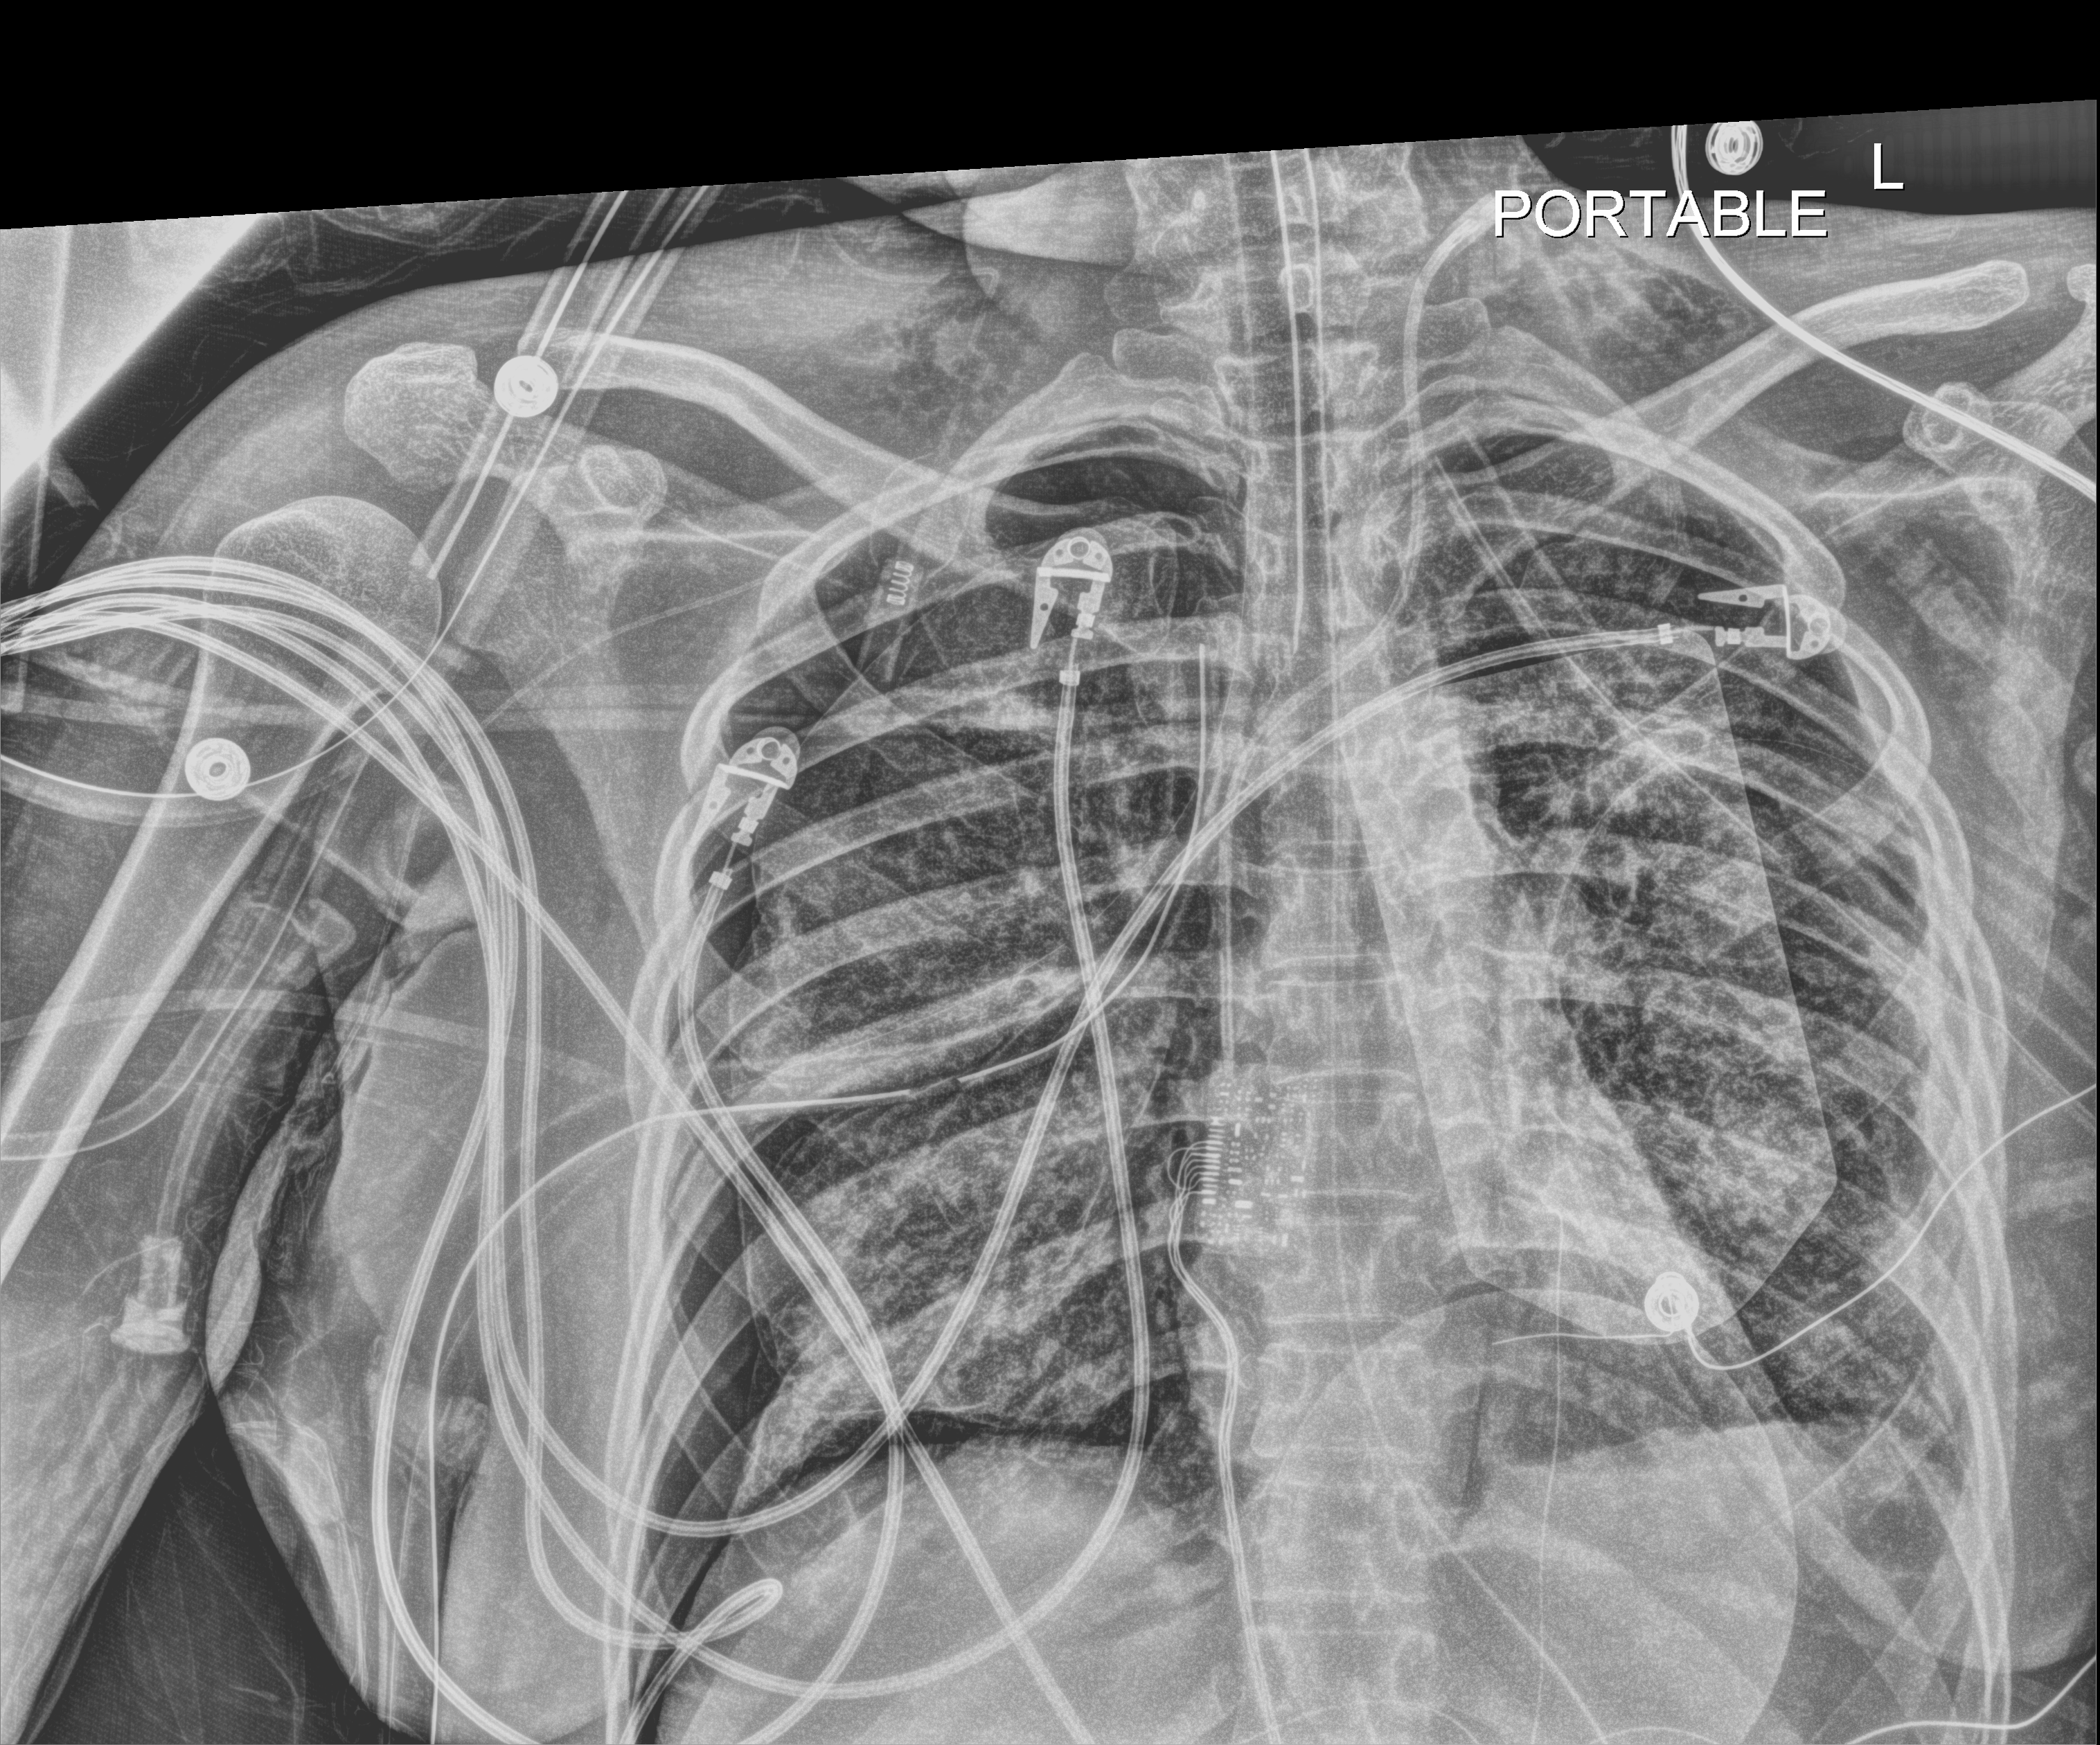
Portable chest radiograph; anteroposterior (AP) projection. Patient hospitalised with COVID-19, aged 18–59 years.
Hospital-stay facts (about this admission, not read from this image; timing relative to this image not recorded):
- chronic kidney disease (admission record): no
- admitted to intensive care during this hospital stay: yes
- smoking status (admission record): never